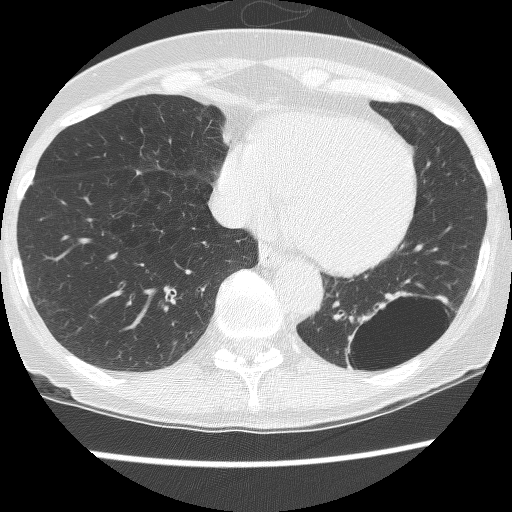
Low-dose screening chest CT, axial slice; third screening round (two years after baseline); lung window (W 1500 / L -600 HU); 2.5 mm slice thickness; lung (sharp) reconstruction kernel (BONE); 120 kVp; 512 × 512 image matrix, field of view 290 × 290 mm. Female, age 61 years at enrolment. Current smoker at enrolment.
Expert reader's lesion annotation, box from (x=333, y=292) to (x=446, y=388) px. The screening reader recorded 2 non-calcified nodules or masses ≥4 mm on this exam (left lower lobe, left lower lobe); which of them this box marks is not recorded. Lung cancer was diagnosed 166 days after this screen: non-small cell carcinoma, left lower lobe, poorly differentiated (G3), stage IB (AJCC 6th edition), 100 mm at pathology.